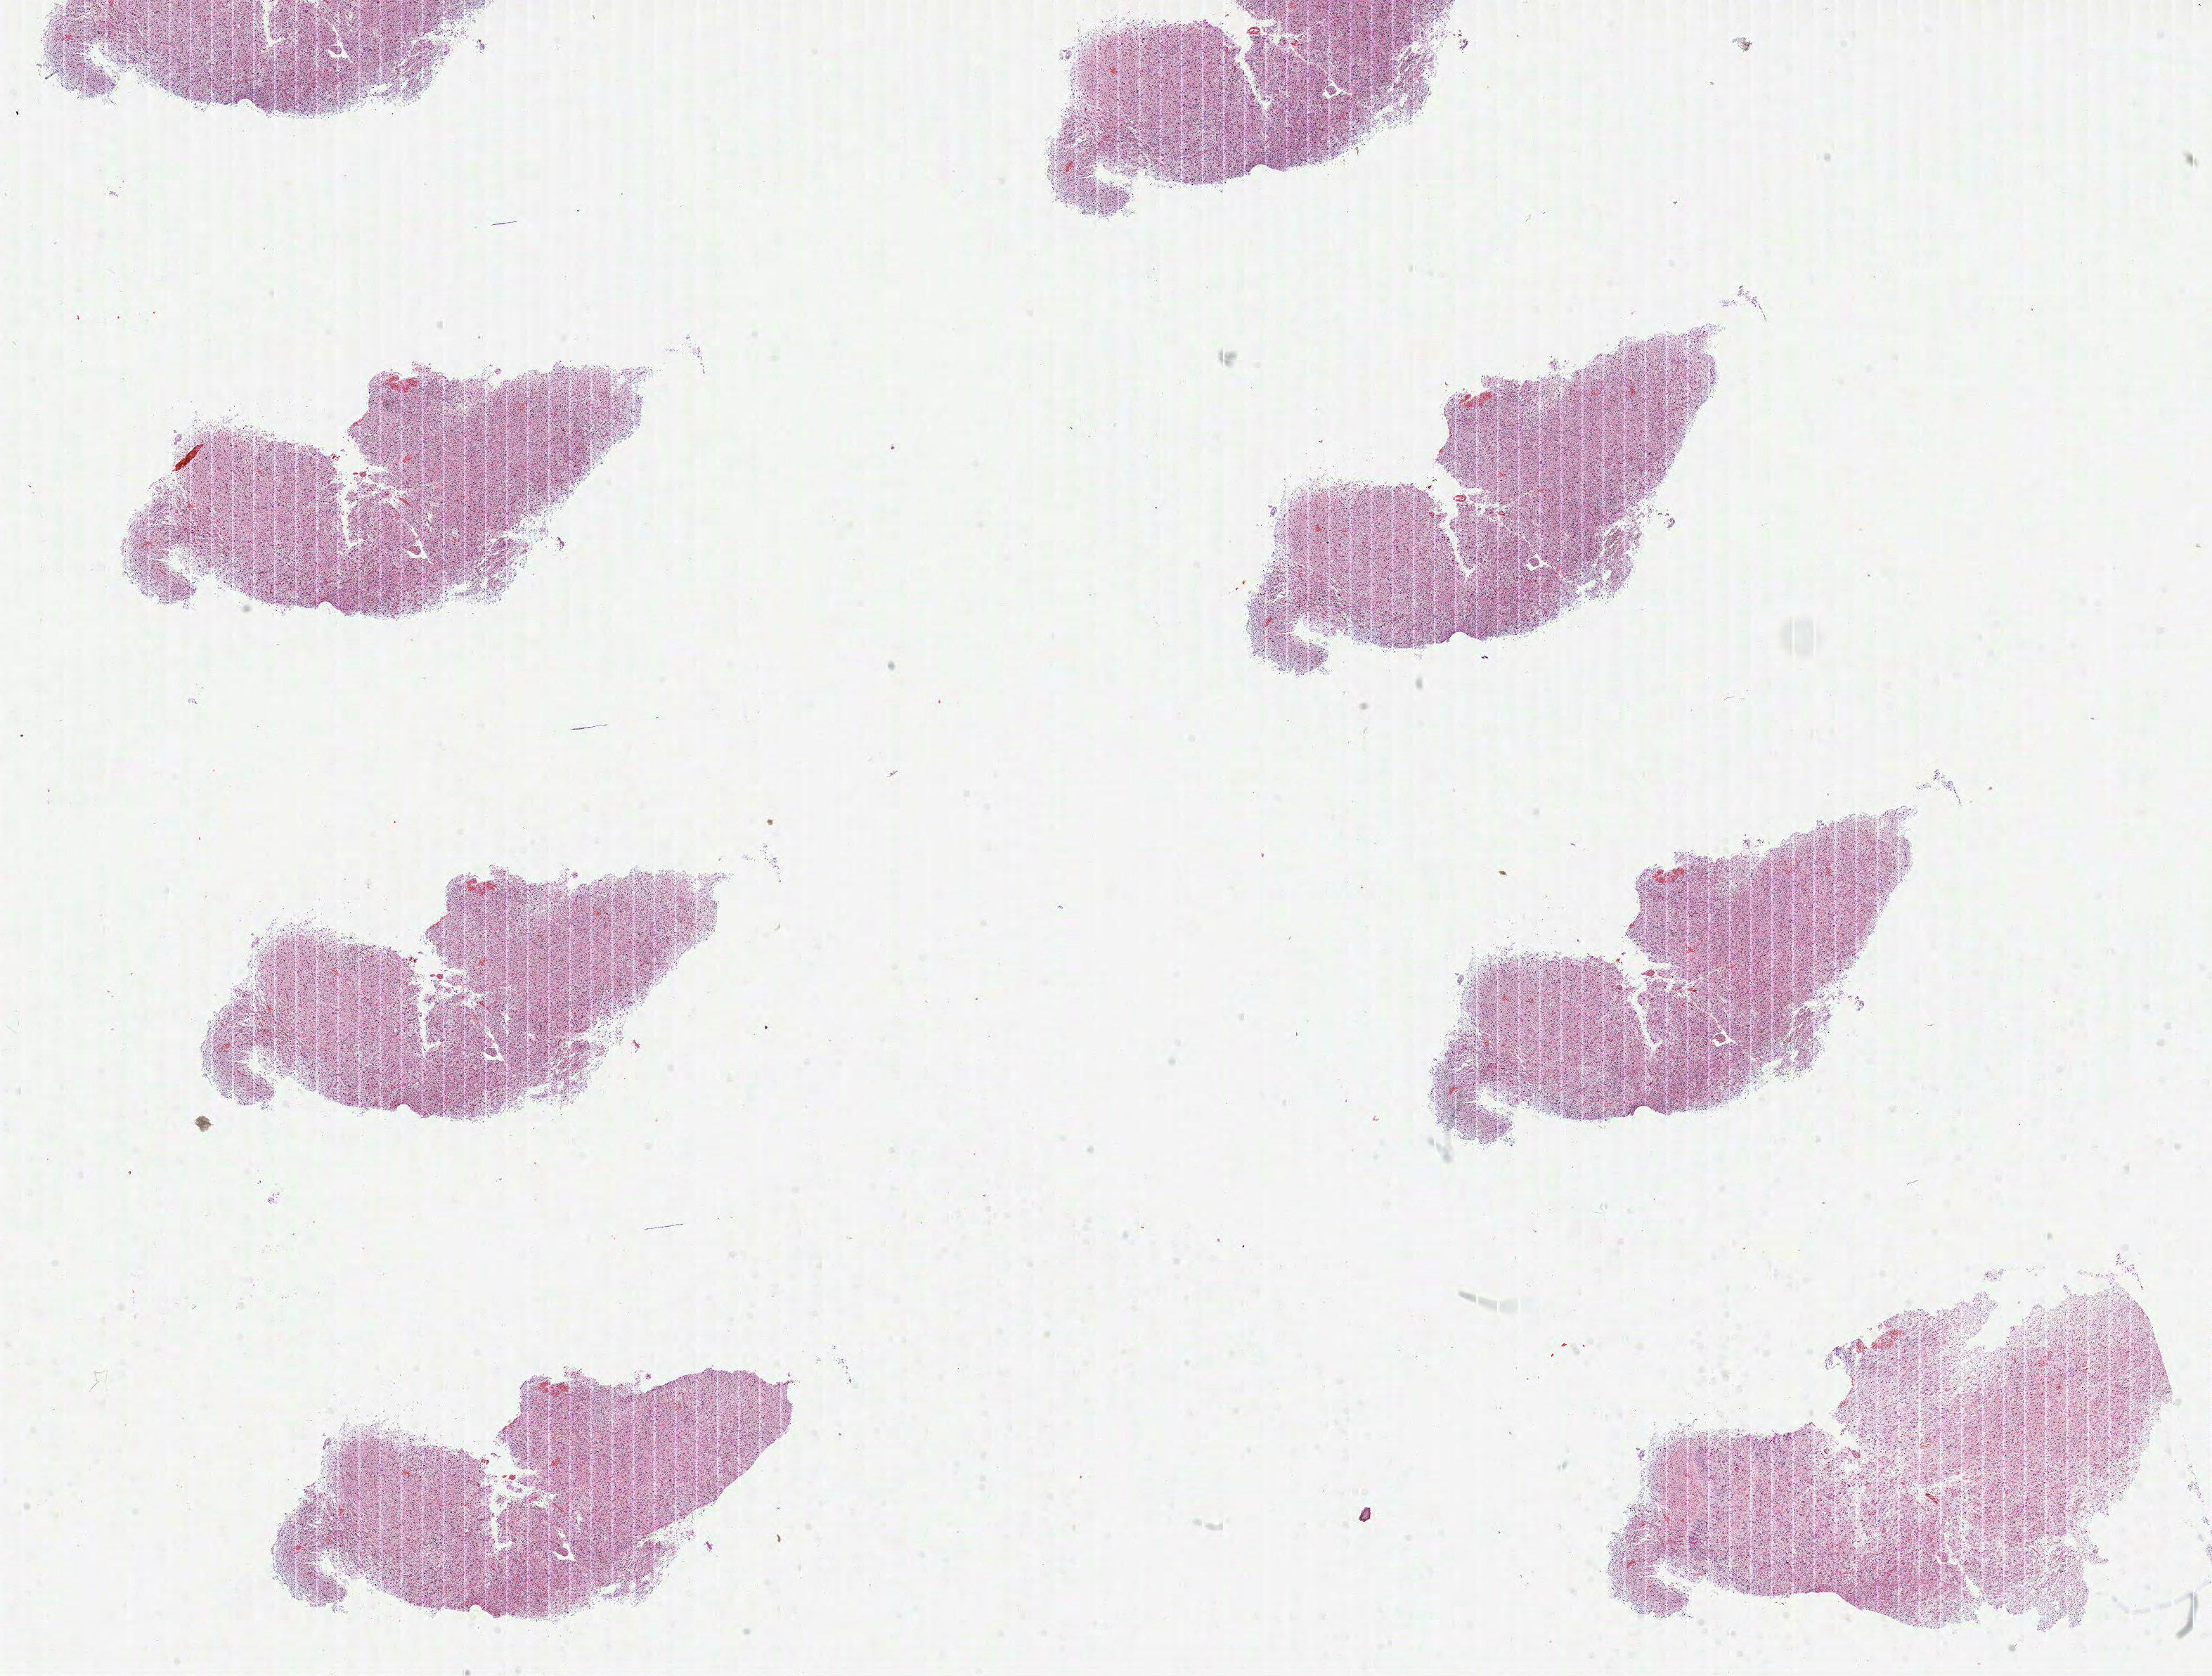
Digitized H&E tissue section (whole slide), low-resolution overview of the scanned area, about 25.4 x 19.2 mm (slide scanned at 40x); formalin-fixed paraffin-embedded (FFPE) diagnostic section; primary tumour sample from the brain. Female, age 49 years at initial diagnosis.
Pathologic diagnosis: Glioblastoma.